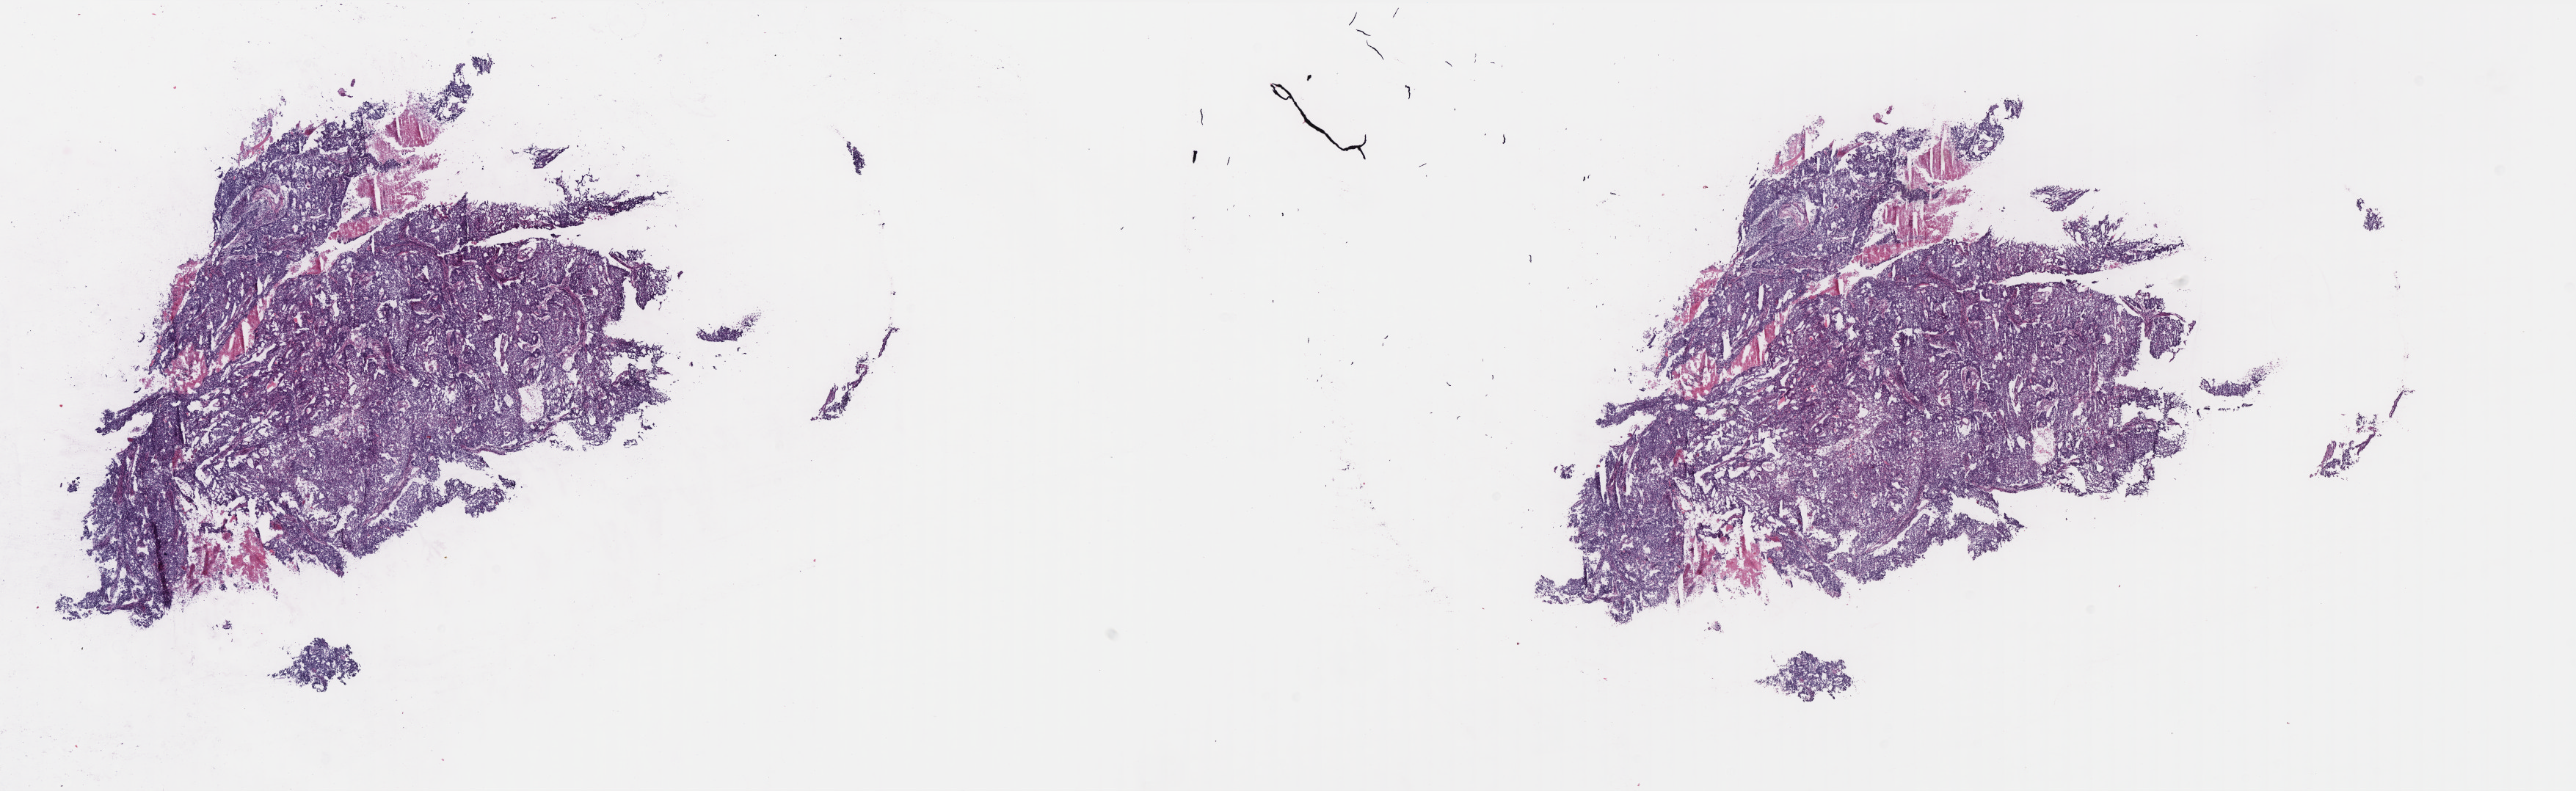
Digitized H&E tissue section (whole slide) — whole scanned area (about 28.1 x 8.6 mm, from a 40x scan) shown as a low-resolution overview; frozen section from the top of the tissue portion; primary tumour sample from the uterus. Female, age 57 years at initial diagnosis. Histologic grade: G2 (moderately differentiated). Composition of this section per pathologist review: tumour cells 90%, tumour nuclei 85%, normal cells 0%, stromal cells 0%, necrosis 10%. Infiltration values recorded for this section: lymphocyte infiltration 0%, monocyte infiltration 0%, neutrophil infiltration 0%.
FIGO stage: IB. Lymph nodes positive (case pathology): 0 of 7 examined. Histologic diagnosis: Endometrioid adenocarcinoma, NOS (endometrium).